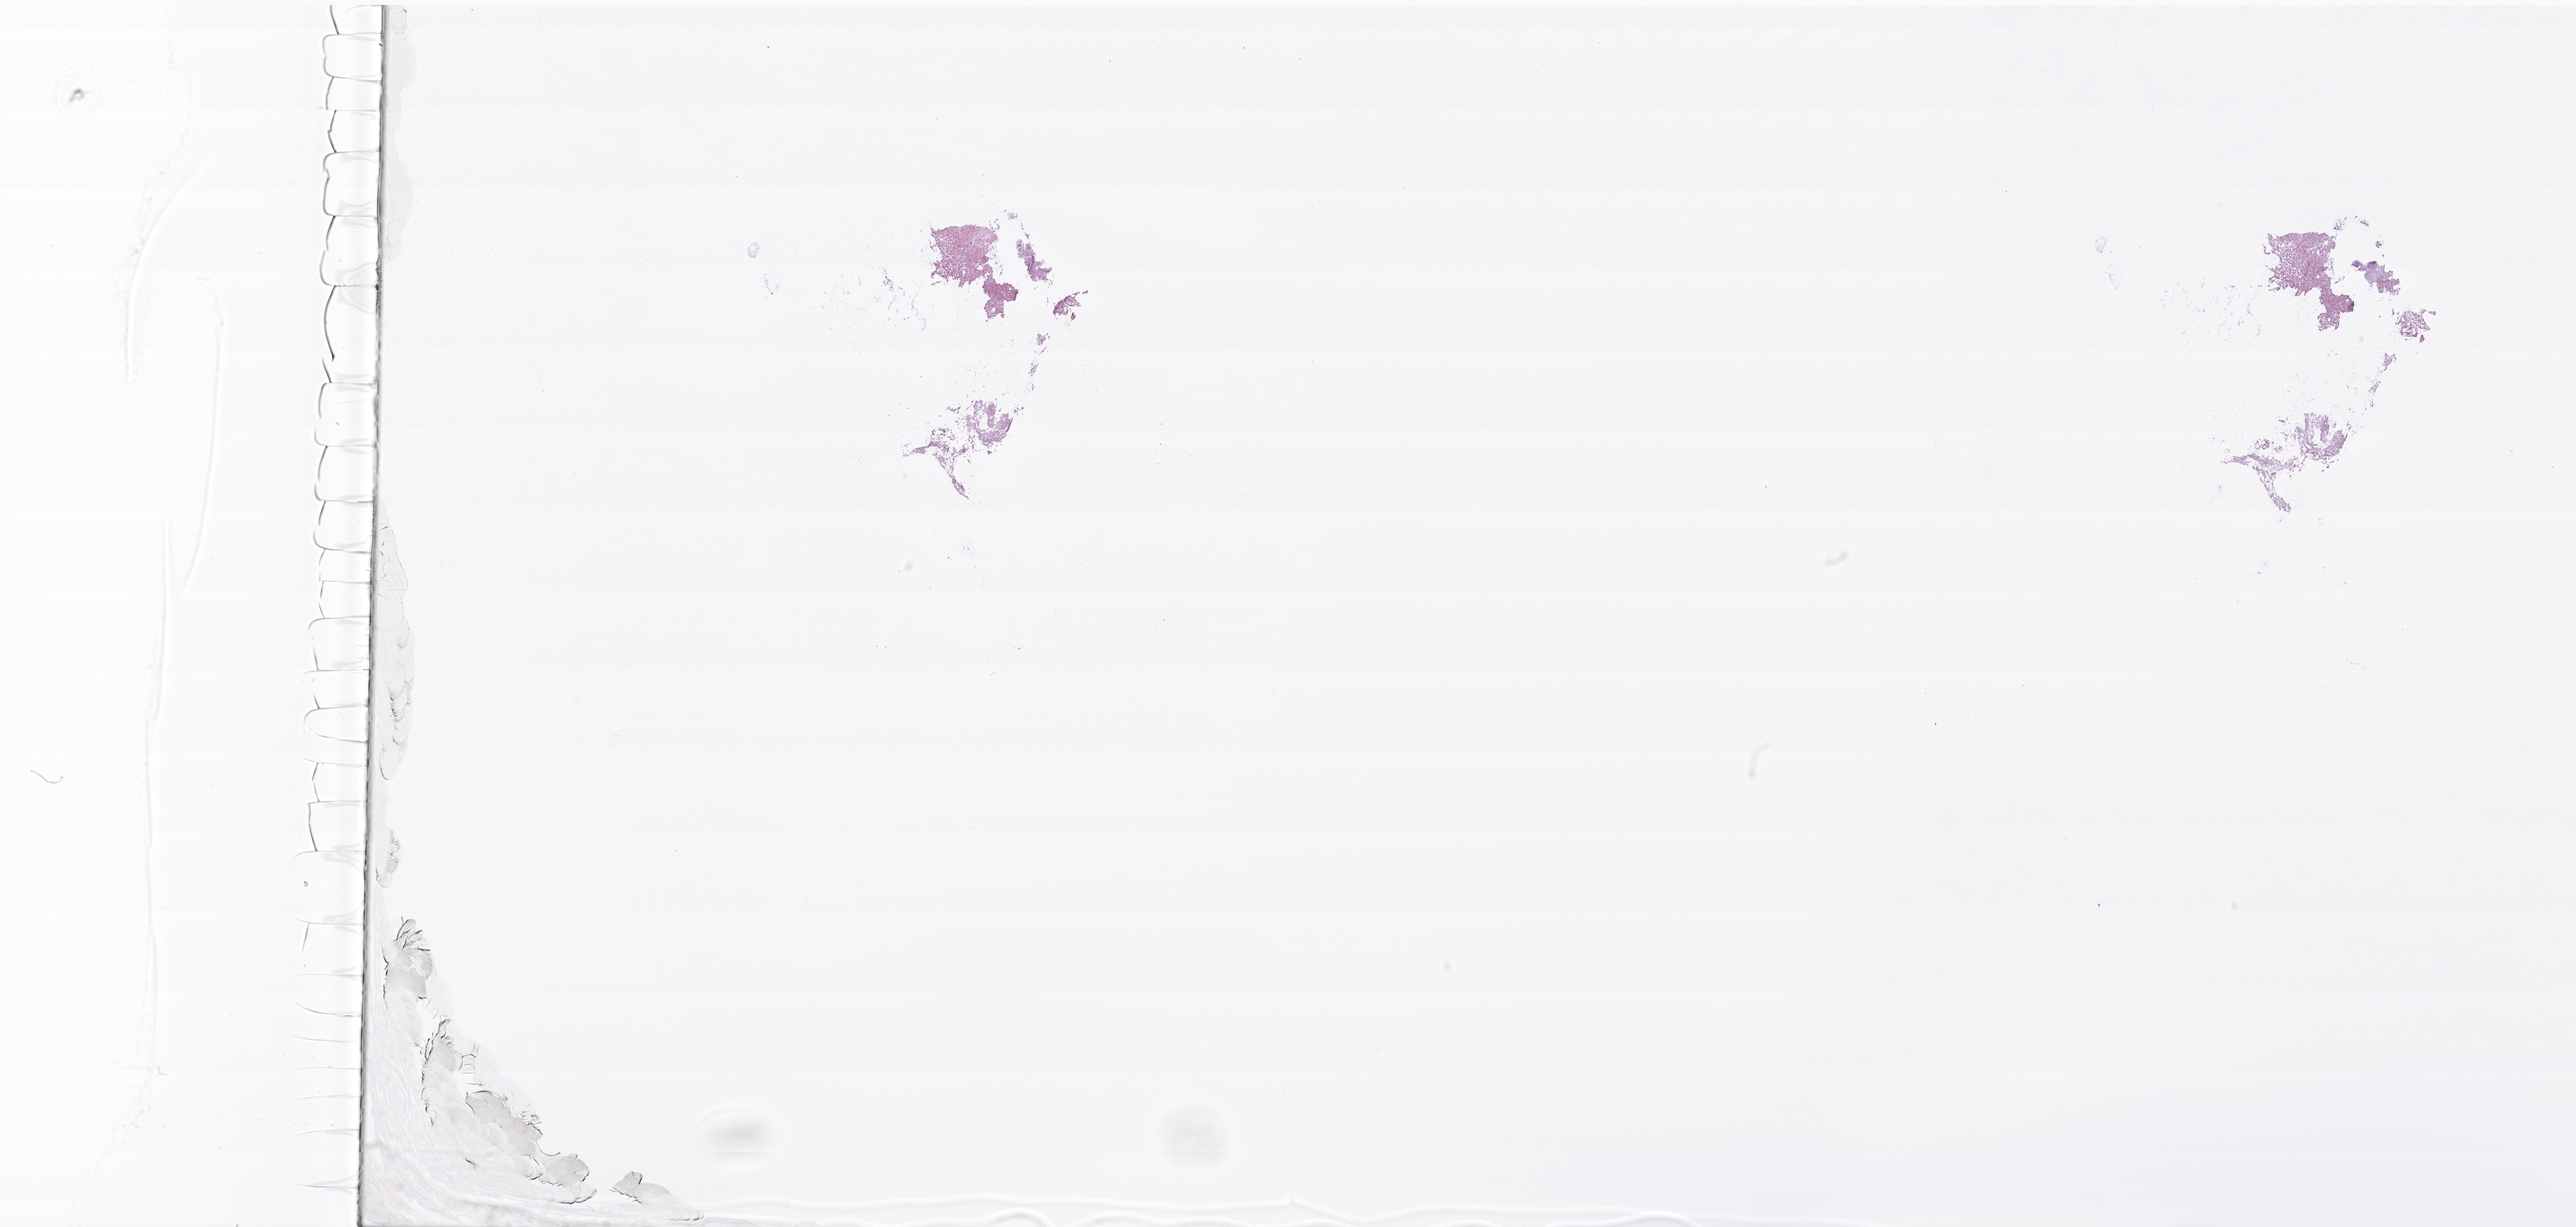
Hematoxylin and eosin (H&E) whole-slide image of tumor tissue from the brain stem, whole scanned area (about 34.2 x 16.3 mm) shown as a low-resolution overview; cryosection (OCT / tissue freezing medium). Male patient, age 184 months.
Diagnosis: Pilocytic astrocytoma.